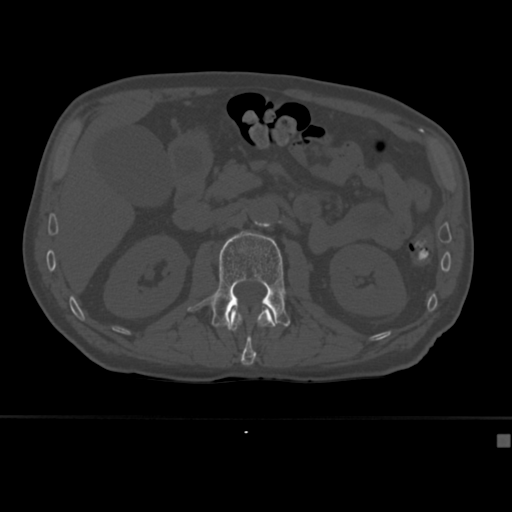
CT including the spine, one axial slice; position 155 of 430 along the scan axis; reconstruction kernel Br40s; 120 kVp; bone window (W 1800 / L 400 HU); 512 × 512 image matrix. Male patient, age 64 years. Case-level facts recorded for this patient, not image findings: primary cancer: uterus; vertebrae with lytic lesions (as recorded): T1, T4, T5, T7, L5.
Annotated regions visible in this slice (semi-automatic segmentation, software-assisted and operator-edited):
- L1 vertebra: box from (x=230, y=306) to (x=276, y=365) px
- L2 vertebra: (x=187, y=231)–(x=290, y=330)